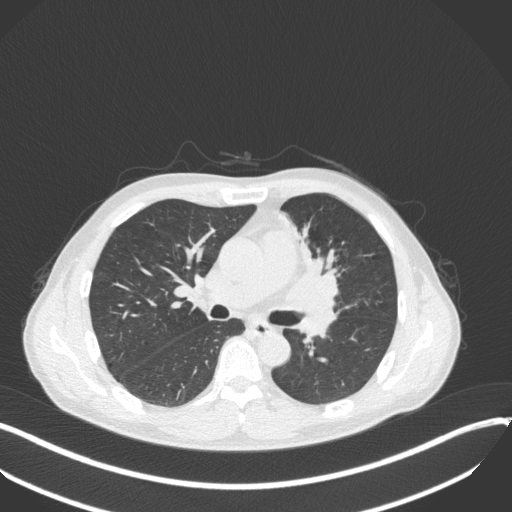
Chest CT, one axial slice; reconstruction kernel B31f; 120 kVp; lung window (W 1500 / L -600 HU); 1 mm slice thickness; 512 × 512 image matrix, field of view 400 × 400 mm. Male patient, age 56 years. From the clinical record (not read from this slice): clinical TNM (as recorded): T2a N0 M0.
Outlined on this slice (rectangle marked by the reading radiologist):
- lung tumour (recorded histology: squamous cell carcinoma): bounding box <277,232,344,318> (left, top, right, bottom; pixels)